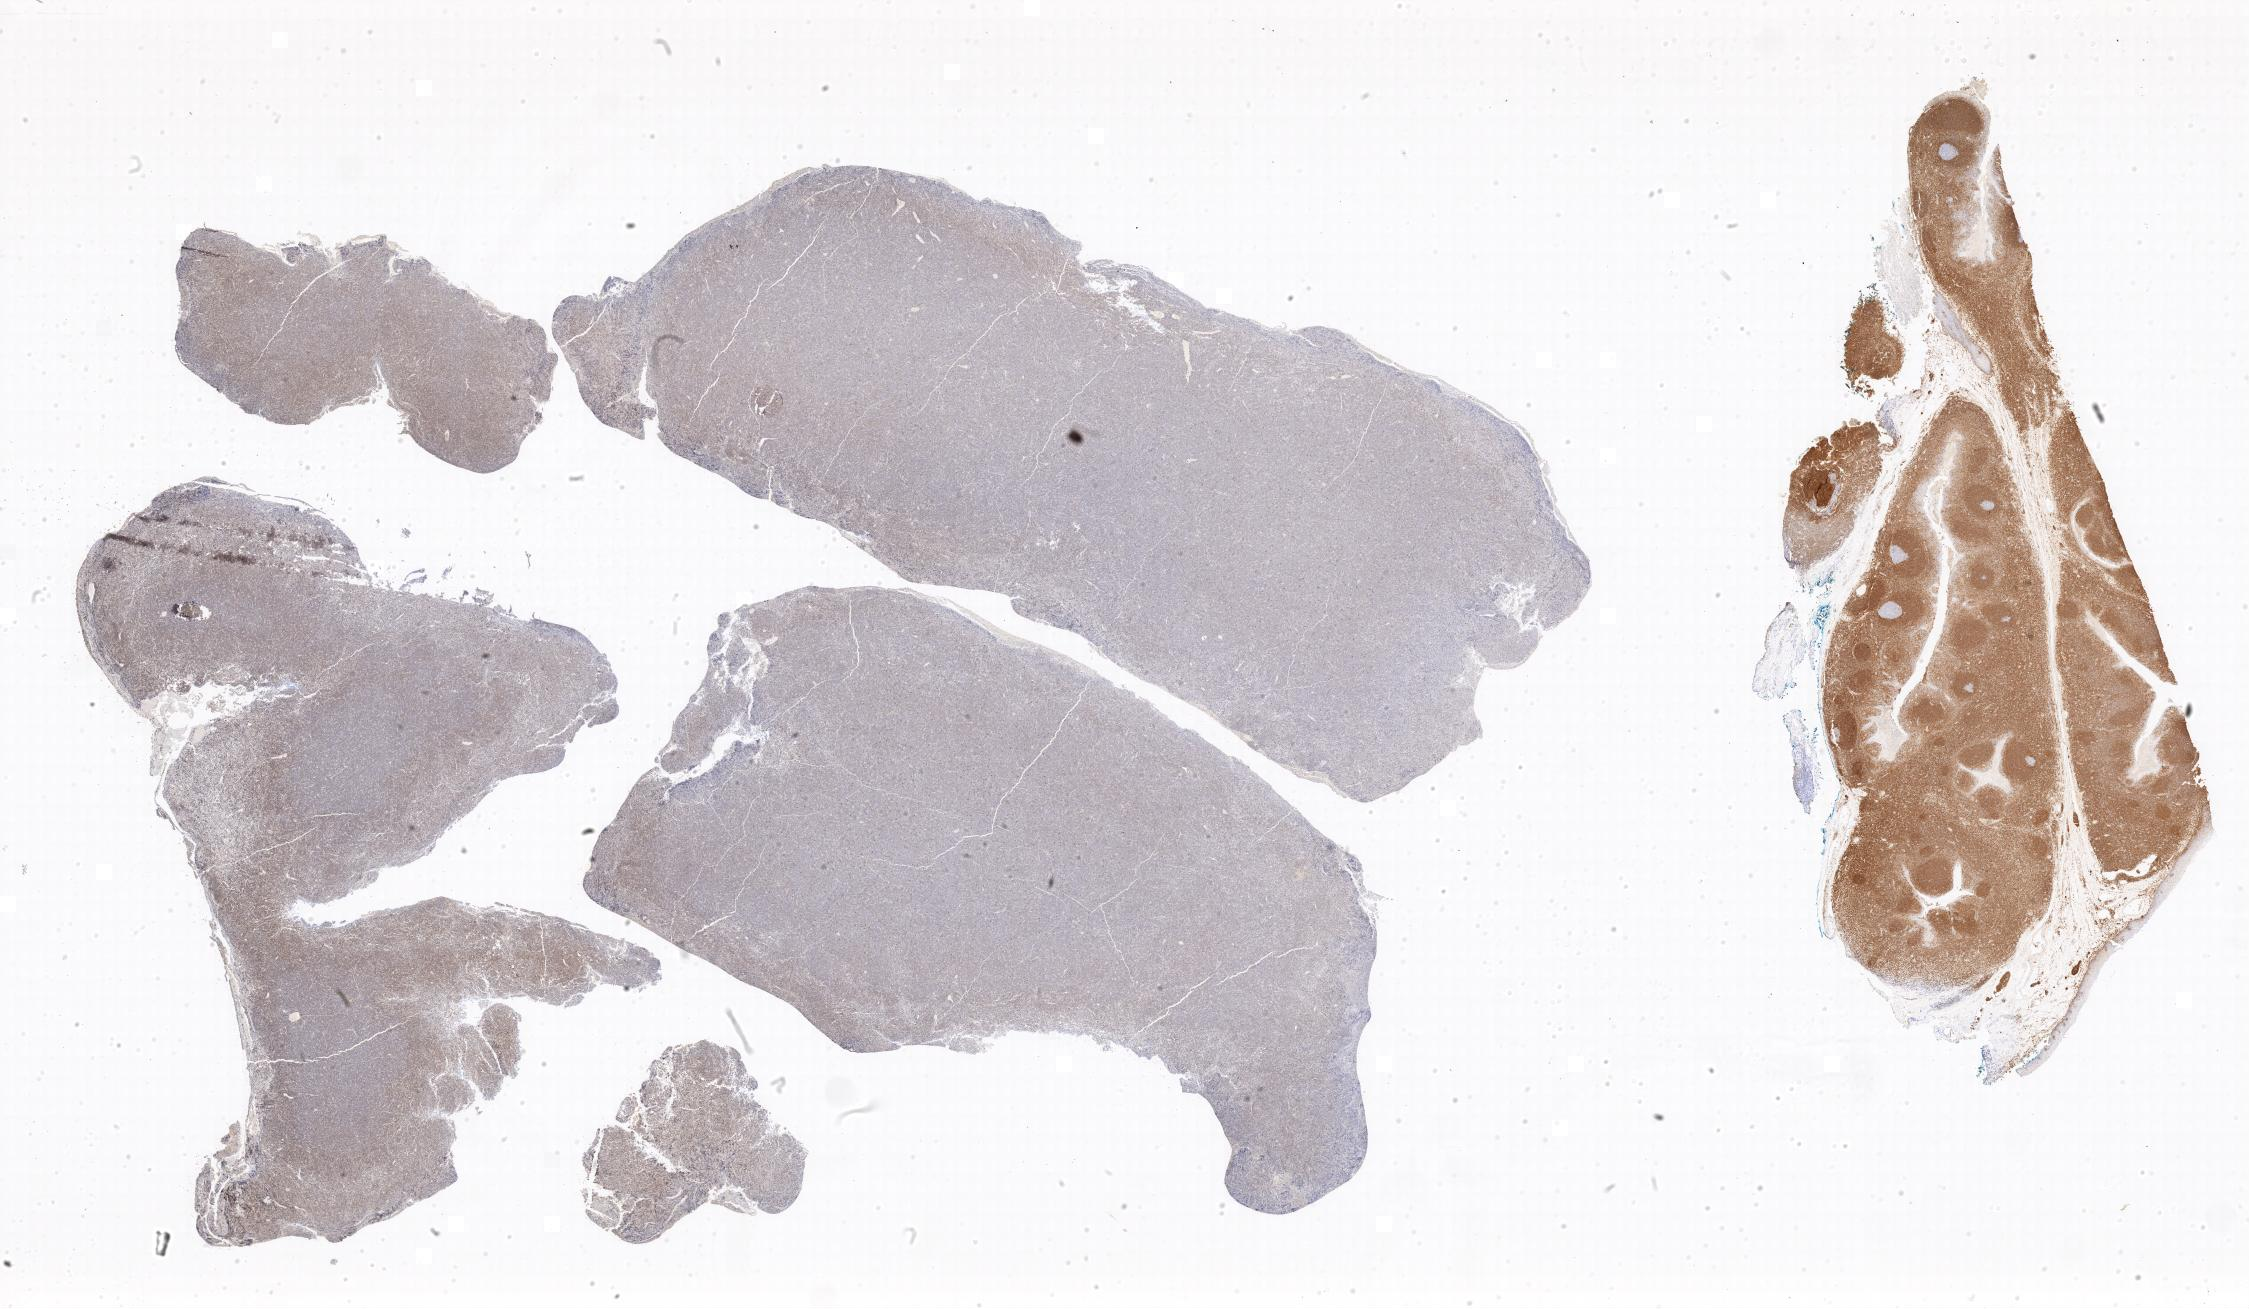
Whole-slide image, immunohistochemical stain for BCL2, low-resolution overview of the scanned area, tumor tissue, anatomic site: peritoneum. Female, age 7 years at initial diagnosis.
- diagnosis: Burkitt lymphoma, NOS